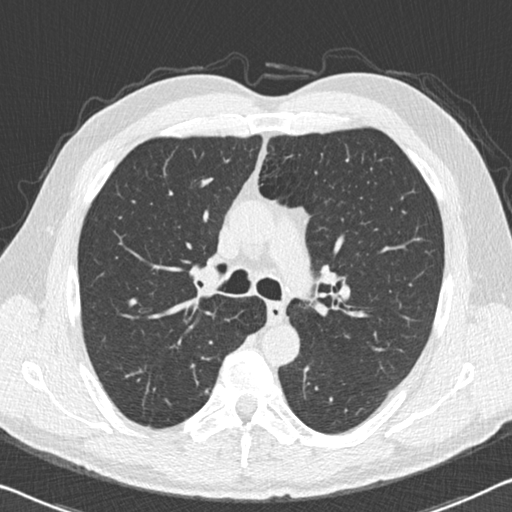
Chest CT (low-dose screening protocol), one axial image. Second annual screen. Lung window (W 1500 / L -600 HU). 2 mm slice thickness. 512 × 512 image matrix, field of view 332 × 332 mm. Male participant, aged 55 years at enrolment. Current smoker at enrolment.
- Lesion marked by an expert reader, bounding box <194,375,223,406> (left, top, right, bottom; pixels).
- No non-calcified nodule or mass ≥4 mm was recorded by the screening reader at this exam.
- Participant outcome: lung cancer diagnosed 641 days after this screen (after the third annual screen) — adenocarcinoma, NOS, right upper lobe, poorly differentiated (G3), stage IA (AJCC 6th edition), 15 mm at pathology.